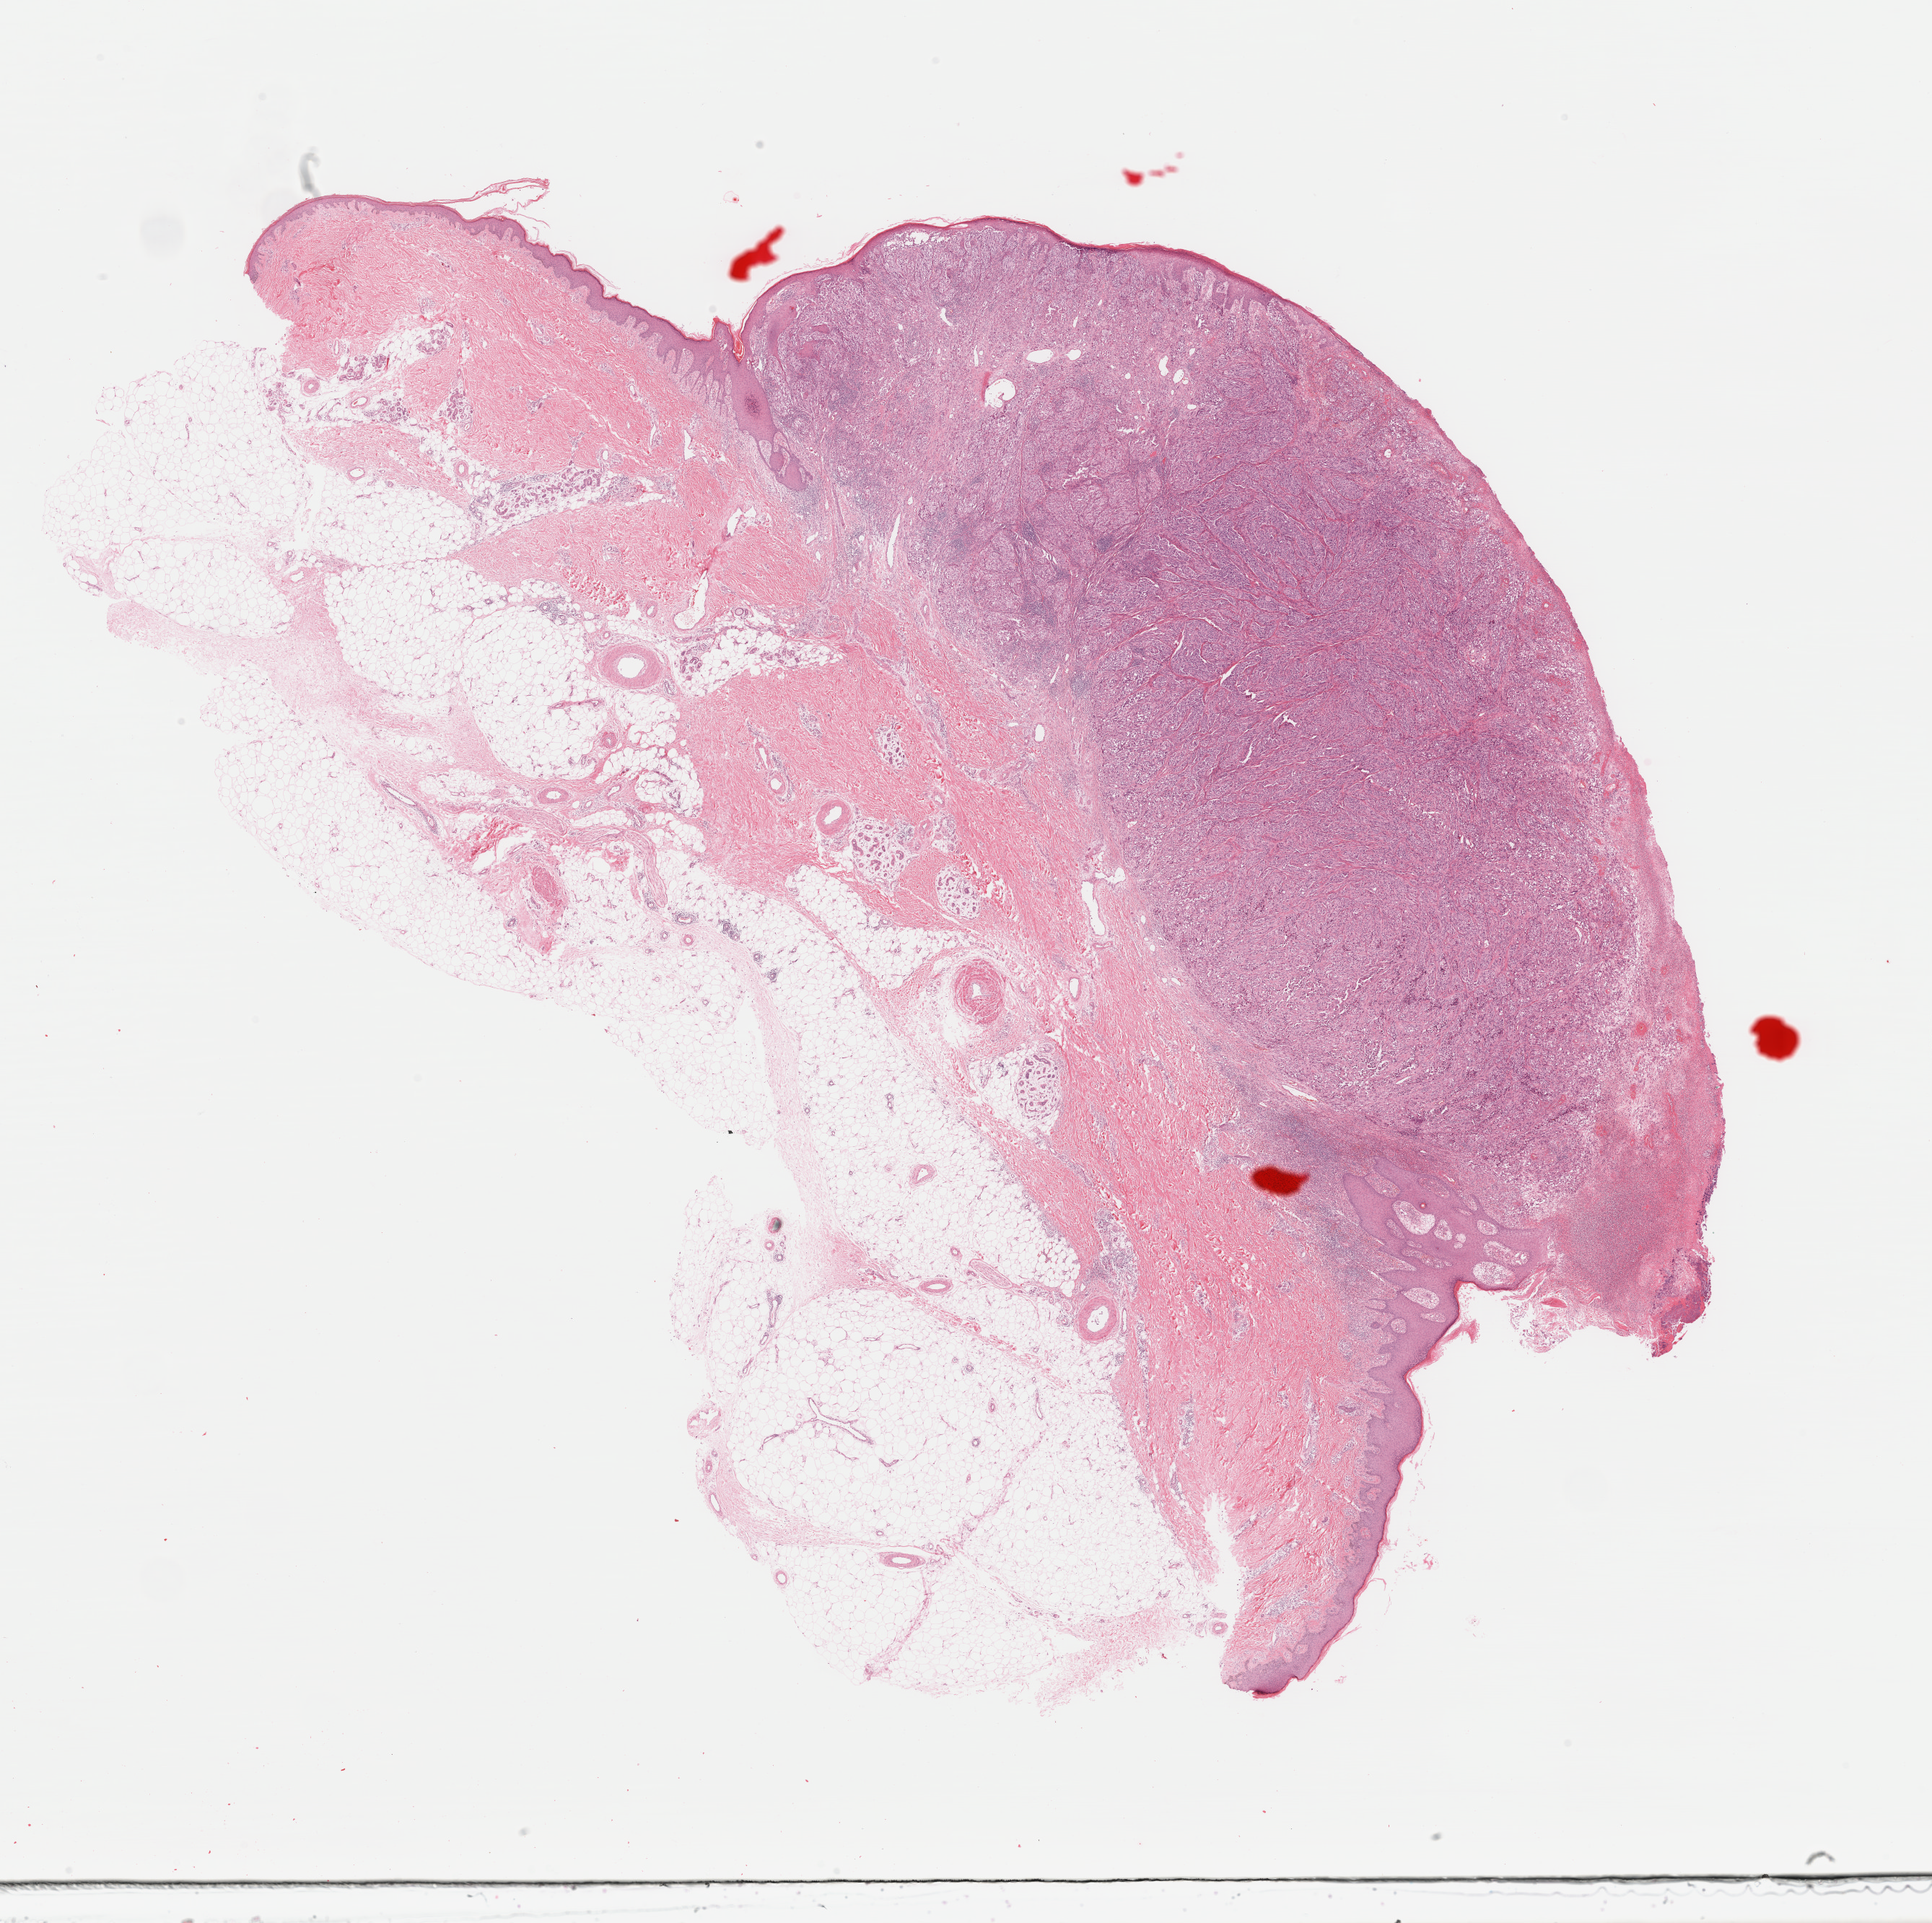
Whole-slide histology image, H&E-stained — whole scanned area (about 21.1 x 21.0 mm) shown as a low-resolution overview, formalin-fixed paraffin-embedded (FFPE) diagnostic section, primary tumour sample from the skin. Female, age 56 years at initial diagnosis.
- histologic diagnosis: Malignant melanoma, NOS
- AJCC pathologic stage: IIC (7th edition)